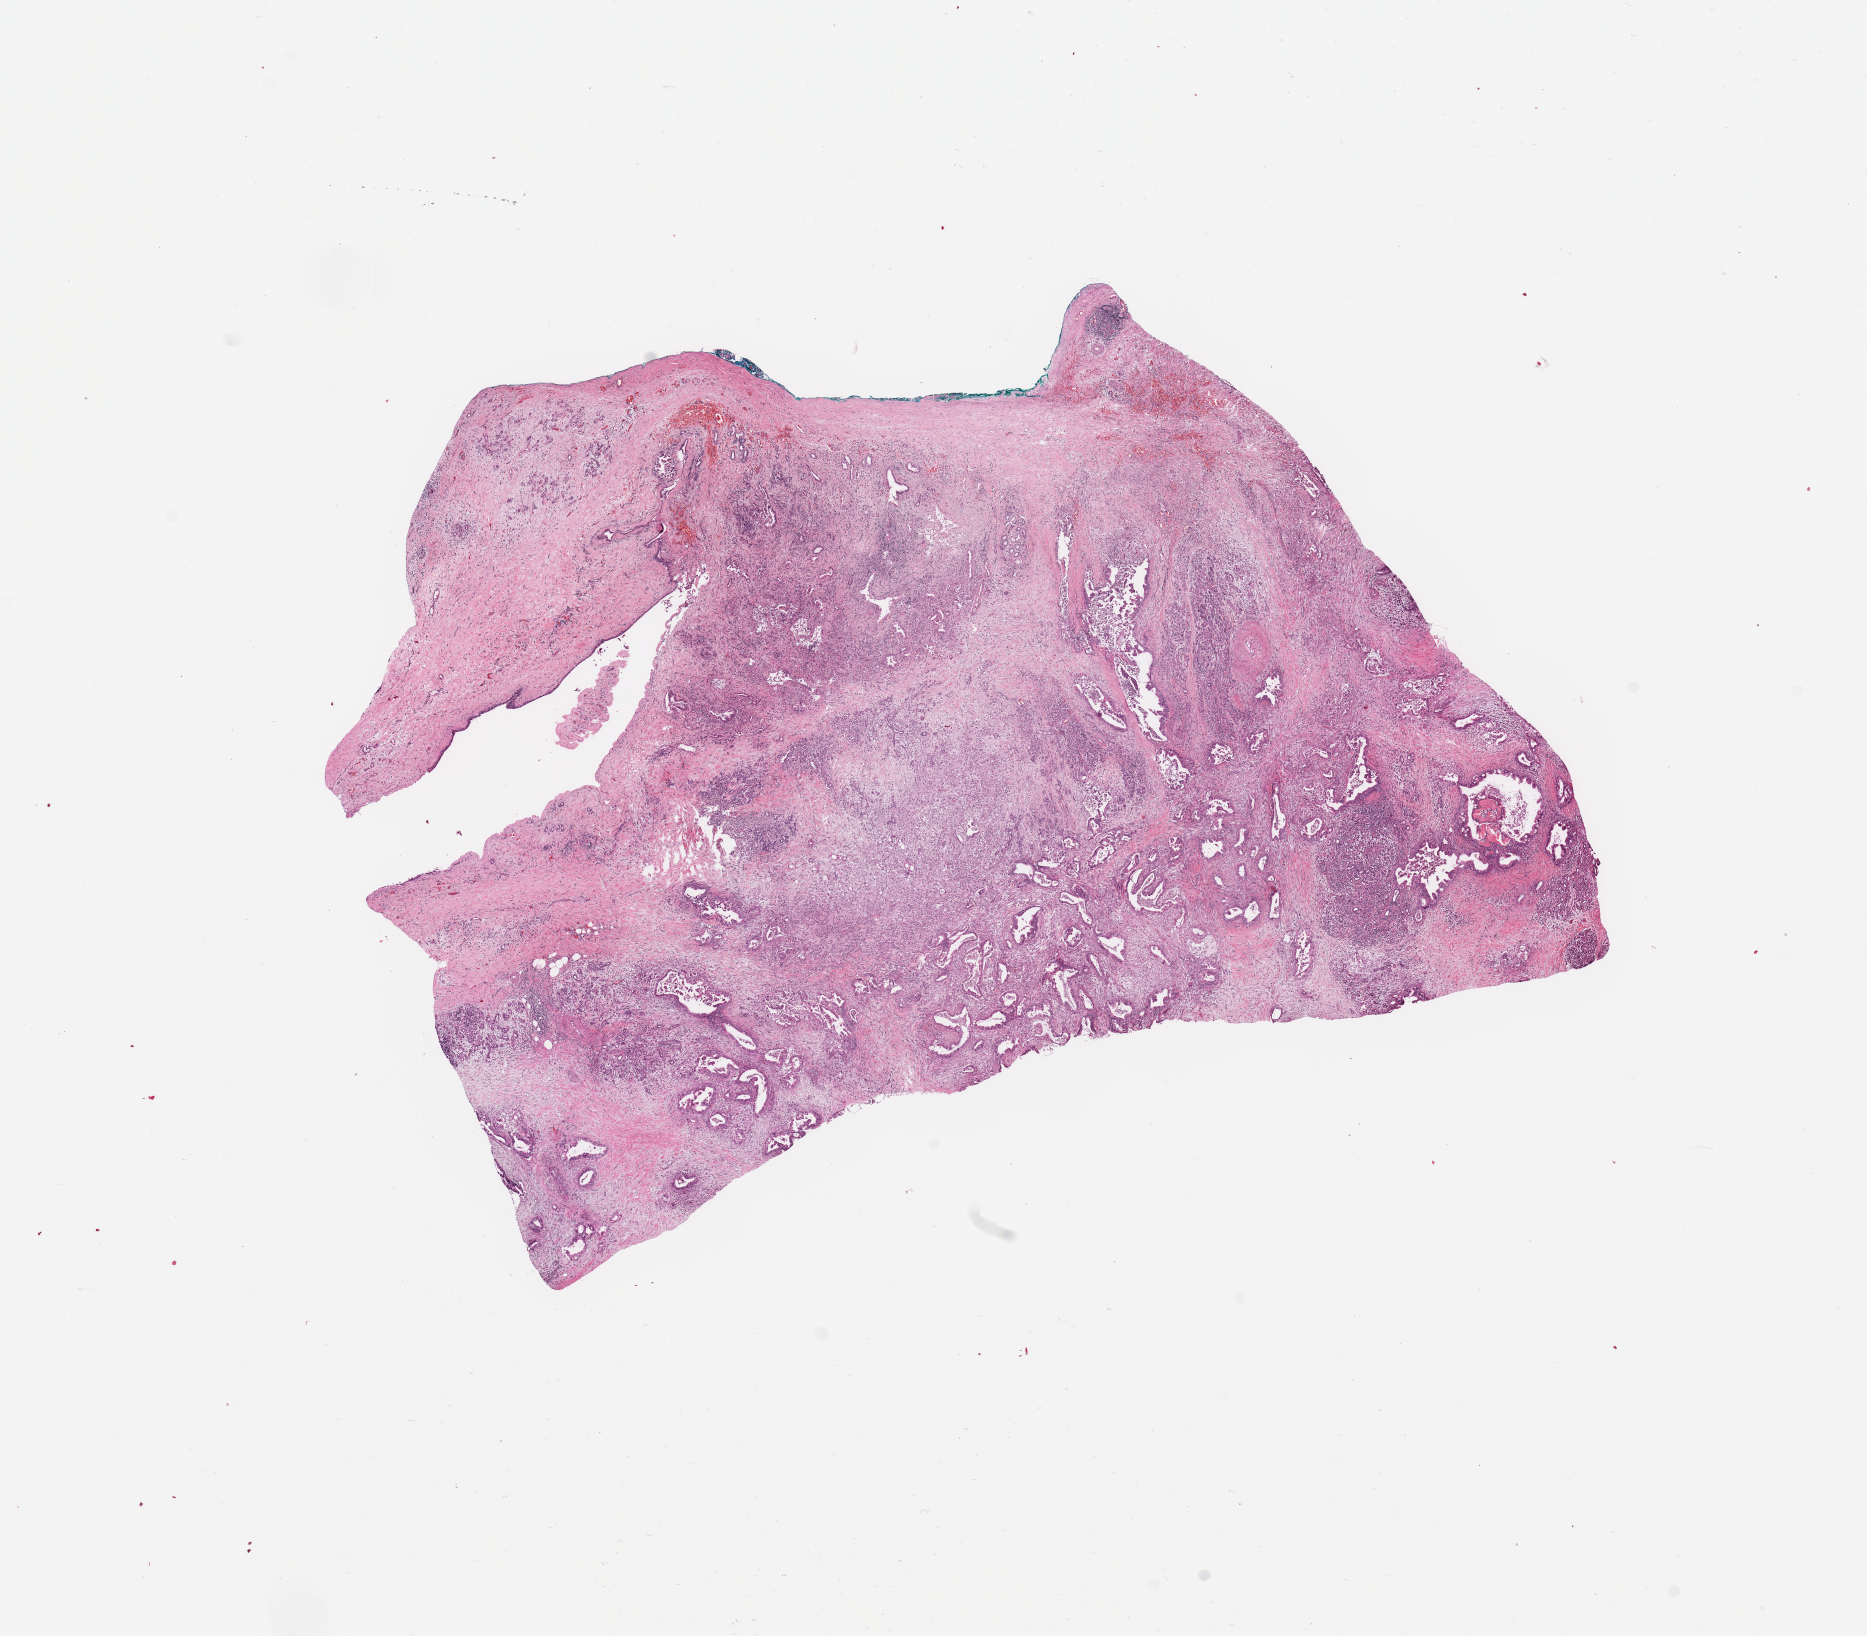
Digitized H&E tissue section (whole slide), low-resolution overview of the scanned area, about 14.8 x 12.9 mm (slide scanned at 20x); tumour tissue sample, sampled site: pancreas. 76-year-old female patient.
Histologic diagnosis: Infiltrating duct carcinoma, NOS.